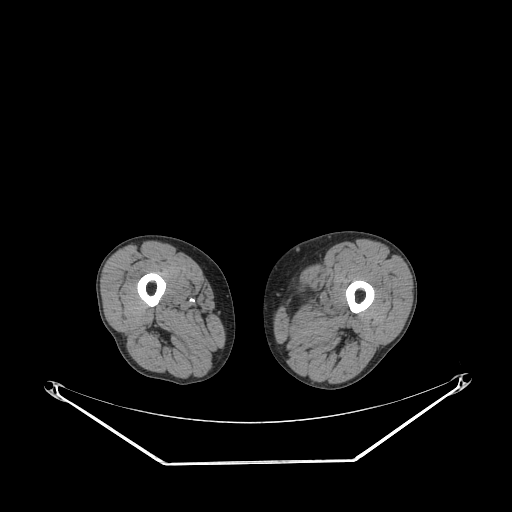
CT of an extremity soft-tissue mass (from a PET/CT study), one axial slice; position 223 of 267 along the scan axis; reconstruction kernel STANDARD; 140 kVp; soft-tissue window (W 400 / L 40 HU); 512 × 512 image matrix. Male patient. From the clinical record (not read from this slice): histological type: pleiomorphic liposarcoma; grade: high; site of the primary tumour: left thigh.
Outlined on this slice (expert contour drawn on MRI and transferred to this co-registered scan by the dataset authors):
- gross tumour volume including surrounding oedema: bounding box (x1, y1, x2, y2) in pixels: (308, 285, 334, 314)